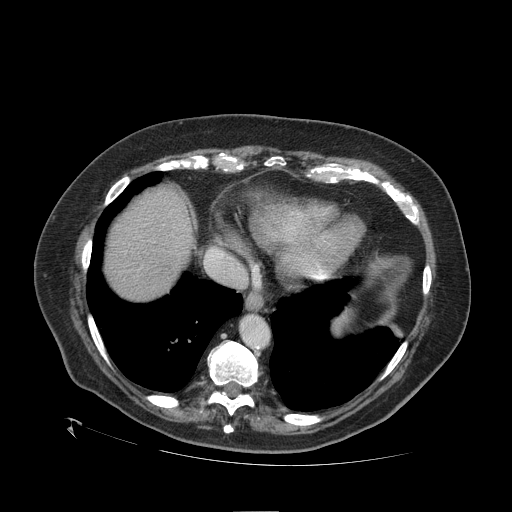
Contrast-enhanced abdominal CT (liver protocol), one axial slice; position 95 of 109 along the scan axis; one of 2 acquisitions stored at this slice position; soft-tissue window (W 400 / L 40 HU); 2.5 mm slice thickness; 512 × 512 image matrix. From the clinical record (not read from this slice): diagnosis: hepatocellular carcinoma (patient treated with transarterial chemoembolisation; whether this scan precedes or follows treatment is not stated here); TNM stage (as recorded): Stage-I; Child-Pugh class: A; tumour differentiation: no biopsy; tumour nodularity: uninodular.
Structures marked on this image (semi-automatically segmented with operator editing):
- abdominal aorta: bounding box <241,316,269,348> (left, top, right, bottom; pixels)
- liver parenchyma outside the tumour (the mass and vessels are separate outlines, so this box may not span the whole liver): <104,186,192,298>